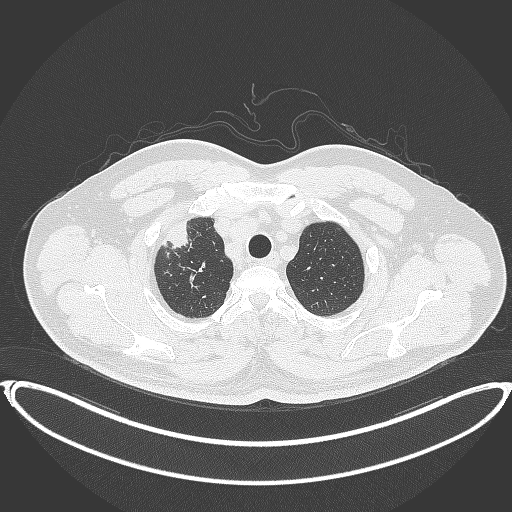
Chest CT, one axial slice. Slice 339 of 399 in the series (ordered by position). Reconstruction kernel B70f. 120 kVp. Lung window (W 1500 / L -600 HU). 1 mm slice thickness. 512 × 512 image matrix, field of view 445 × 445 mm. Male patient, age 53 years. Case-level facts recorded for this patient, not image findings: clinical TNM (as recorded): T2a N0 M0.
Annotated regions visible in this slice (rectangle marked by the reading radiologist):
- lung tumour (recorded histology: adenocarcinoma): bounding box <164,218,193,257> (left, top, right, bottom; pixels)